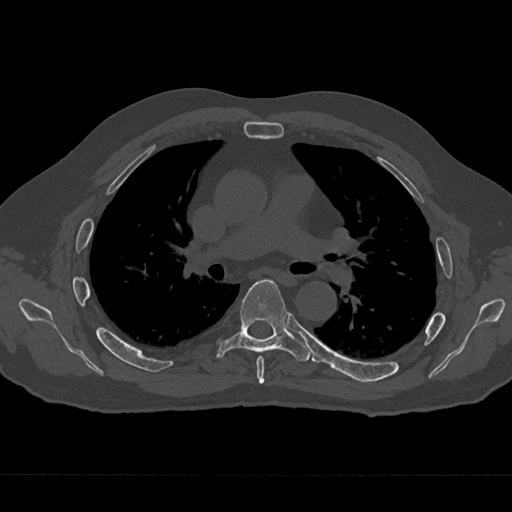
CT including the spine, one axial slice. Position 433 of 797 along the scan axis. Reconstruction kernel Br40s/3. Bone window (W 1800 / L 400 HU). 0.5 mm slice thickness. 512 × 512 image matrix, field of view 377 × 377 mm. Patient: male, 75 years. Case-level facts recorded for this patient, not image findings: primary cancer: renal.
Outlined on this slice (semi-automatic segmentation, software-assisted and operator-edited):
- T5 vertebra: bounding box [x1, y1, x2, y2] px = [256, 356, 265, 384]
- T6 vertebra: [216, 279, 310, 362]